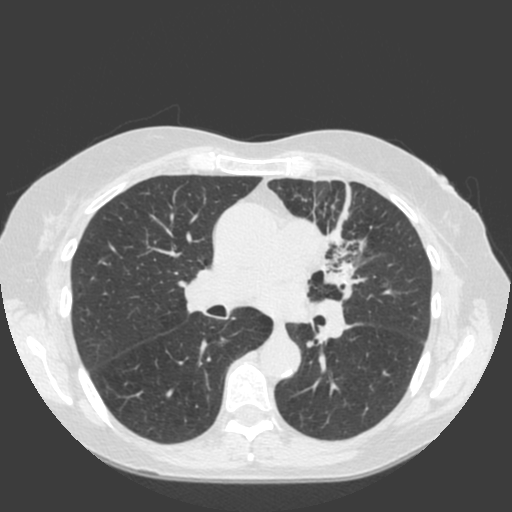
Low-dose screening chest CT, one axial slice; position 109 of 184 along the scan axis; 120 kVp; lung window (W 1500 / L -600 HU); 512 × 512 image matrix.
Annotated regions visible in this slice (manually delineated by an expert):
- lesion 1 (tumor, hilum of left lung): box from (x=317, y=230) to (x=366, y=342) px